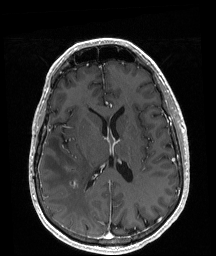
Brain MRI from a brain-tumour surgery series, one axial slice. Position 93 of 208 along the scan axis. T1-weighted post-contrast. 216 × 256 image matrix. Case-level facts recorded for this patient, not image findings: histopathology: Astrocytoma; WHO grade: 4; IDH mutation: yes.
Structures marked on this image (outlined manually by an expert reader):
- tumour: bounding box <74,181,76,186> (left, top, right, bottom; pixels)